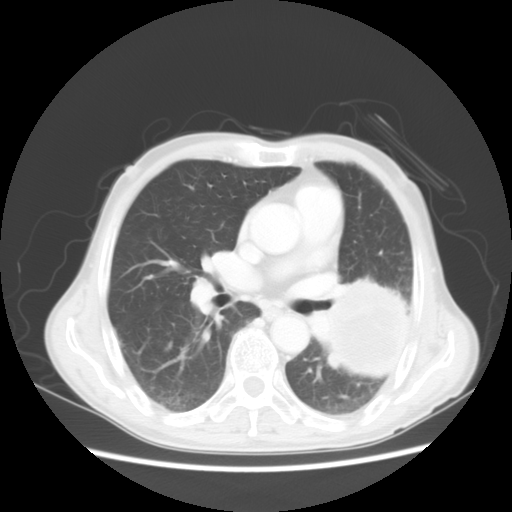
Chest CT, one axial slice; reconstruction kernel STANDARD; lung window (W 1500 / L -600 HU); 5 mm slice thickness; 512 × 512 image matrix, field of view 360 × 360 mm. Male patient, age 64 years. Case-level facts recorded for this patient, not image findings: clinical TNM (as recorded): T4 N0 M0.
Outlined on this slice (bounding box drawn by a radiologist):
- lung tumour (recorded histology: squamous cell carcinoma): bounding box (x1, y1, x2, y2) in pixels: (321, 277, 419, 389)